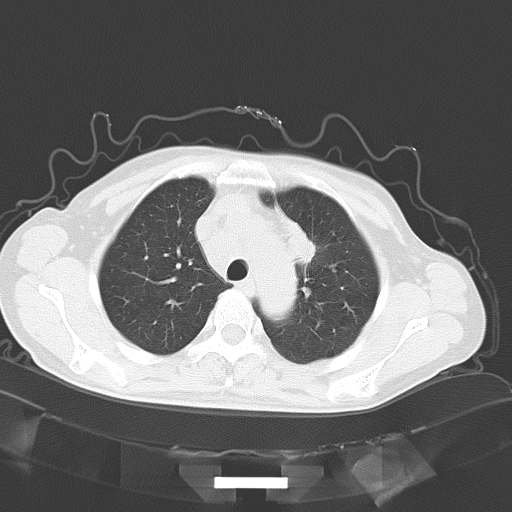
Chest CT, one axial slice. Lung window (W 1500 / L -600 HU). 5 mm slice thickness. 512 × 512 image matrix, field of view 353 × 353 mm. Patient: female, 50 years. From the clinical record (not read from this slice): clinical TNM (as recorded): T2a N1 M1c.
Annotated regions visible in this slice (bounding box drawn by a radiologist):
- lung tumour (recorded histology: adenocarcinoma): box from (x=270, y=200) to (x=320, y=274) px